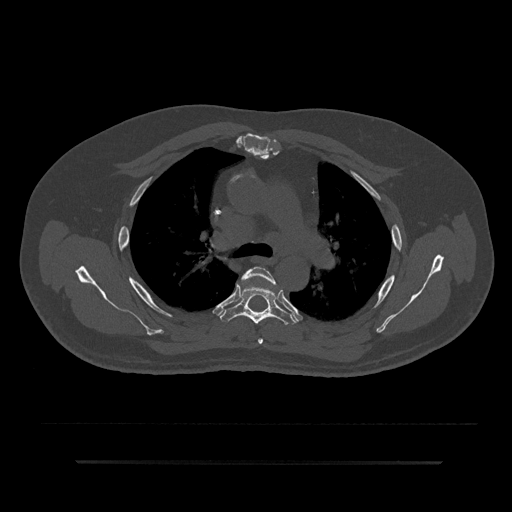
CT including the spine, one axial slice. Position 585 of 797 along the scan axis. Reconstruction kernel Br40s/3. 120 kVp. Bone window (W 1800 / L 400 HU). 0.5 mm slice thickness. 512 × 512 image matrix, field of view 464 × 464 mm. Patient: male, 59 years. Case-level facts recorded for this patient, not image findings: primary cancer: bile ducts; vertebrae with lytic lesions (as recorded): T10.
Annotated regions visible in this slice (semi-automatic segmentation, software-assisted and operator-edited):
- T4 vertebra: box from (x=241, y=266) to (x=277, y=344) px
- T5 vertebra: (x=220, y=285)–(x=297, y=325)